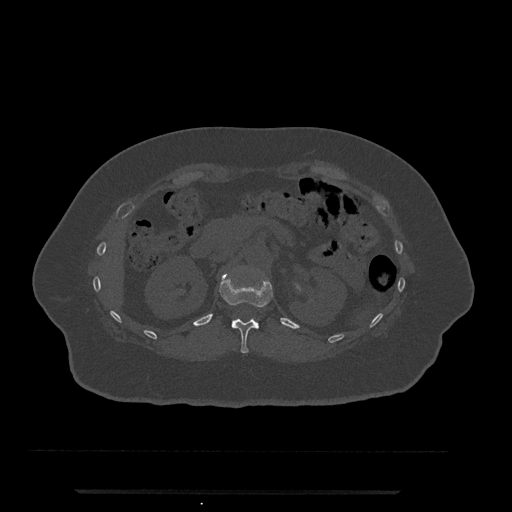
CT including the spine, one axial slice. Position 154 of 797 along the scan axis. Reconstruction kernel Br40s/3. Bone window (W 1800 / L 400 HU). 0.5 mm slice thickness. 512 × 512 image matrix. Female patient, age 51 years. Case-level facts recorded for this patient, not image findings: primary cancer: neuro; vertebrae with lytic lesions (as recorded): T8.
Outlined on this slice (semi-automatic segmentation, software-assisted and operator-edited):
- T12 vertebra: bounding box [x1, y1, x2, y2] px = [219, 273, 273, 353]